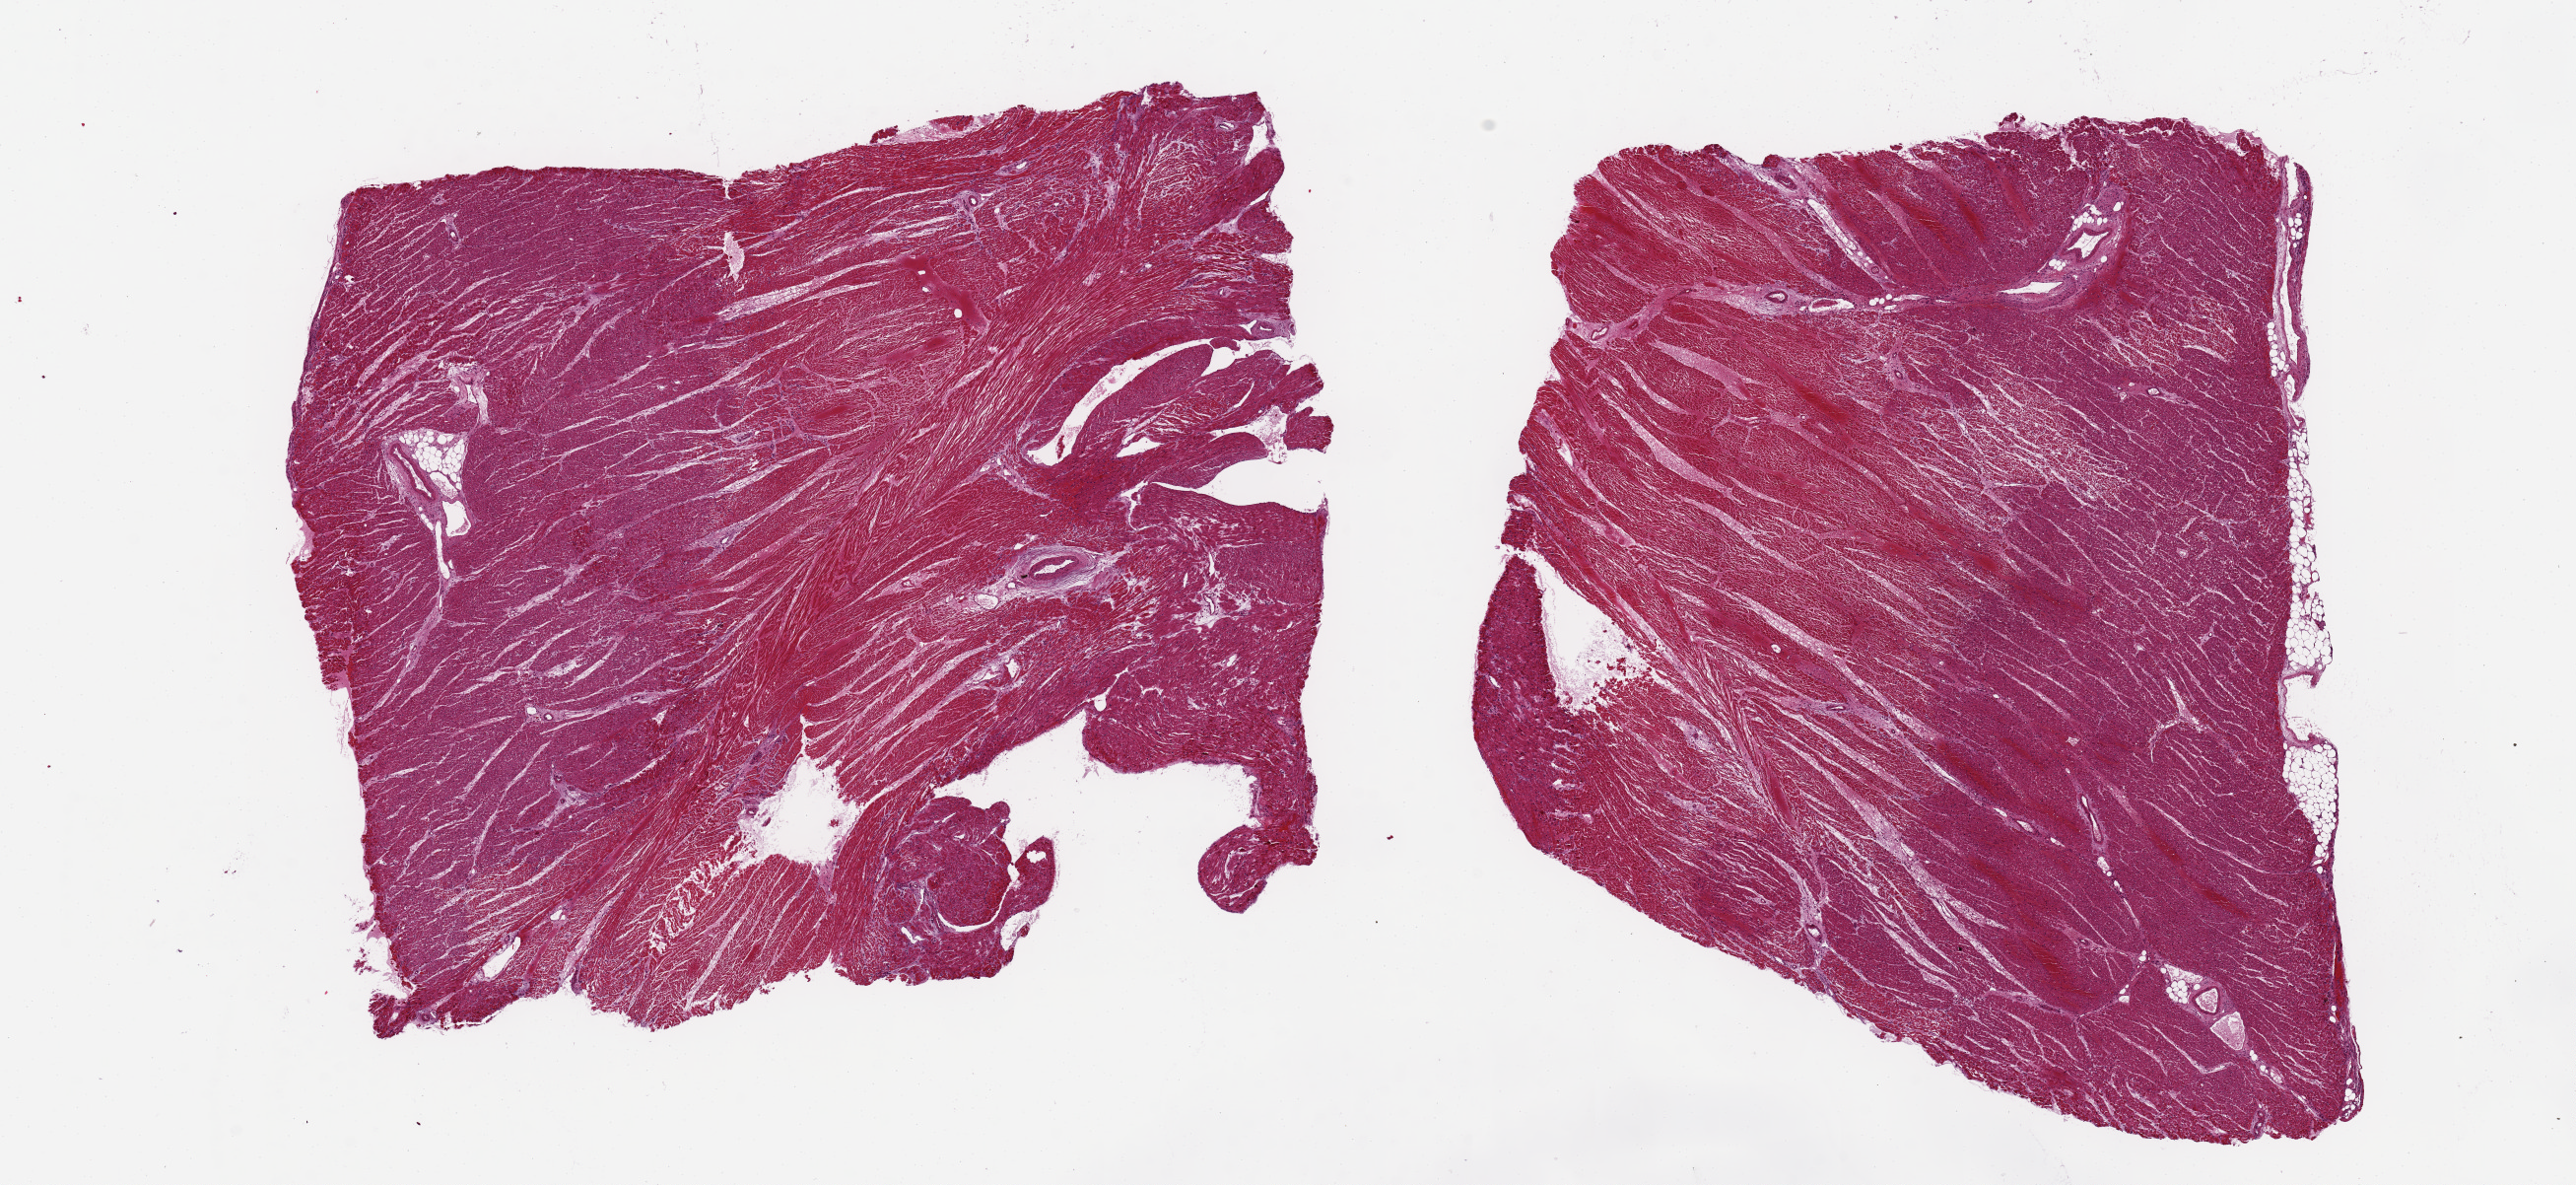
Digitized H&E-stained section, low-resolution overview of the scanned area, about 20.7 x 9.5 mm. PAXgene-fixed paraffin-embedded (PFPE) section. Target tissue: heart. Tissue donor sample. Donor: female.
Pathologist's review note for this sample: 2 aliquots, ~8x6mm.